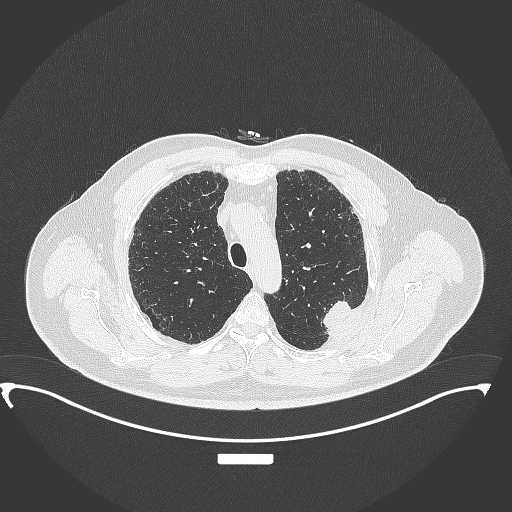
Chest CT, one axial slice; position 277 of 350 along the scan axis; lung window (W 1500 / L -600 HU); 512 × 512 image matrix, field of view 459 × 459 mm. Patient: male, 64 years. From the clinical record (not read from this slice): clinical TNM (as recorded): T1c N1 M1.
Annotated regions visible in this slice (rectangle marked by the reading radiologist):
- lung tumour (recorded histology: adenocarcinoma): box from (x=319, y=294) to (x=357, y=342) px